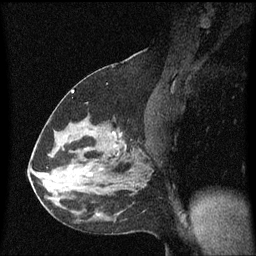
Breast MRI (dynamic contrast-enhanced), one sagittal slice; position 33 of 60 along the scan axis; dynamic contrast-enhanced series, image 2 of 3 at this slice position (ordered by acquisition); 1.5 T; TE 4.2 ms, TR 8.4 ms; 2 mm slice thickness; 256 × 256 image matrix, field of view 200 × 200 mm. Female patient, age 37 years. From the clinical record (not read from this slice): setting: breast cancer imaged before/during neoadjuvant chemotherapy; receptor status: HR-positive, HER2-negative.
Outlined on this slice (semi-automatically segmented with operator editing):
- analysis volume of interest (the breast-tissue region the enhancement analysis was run in; not a lesion): box from (x=95, y=124) to (x=151, y=171) px
- tumour enhancement mask (voxels above the 70 % enhancement threshold inside the analysis volume of interest): (x=123, y=142)–(x=127, y=147)